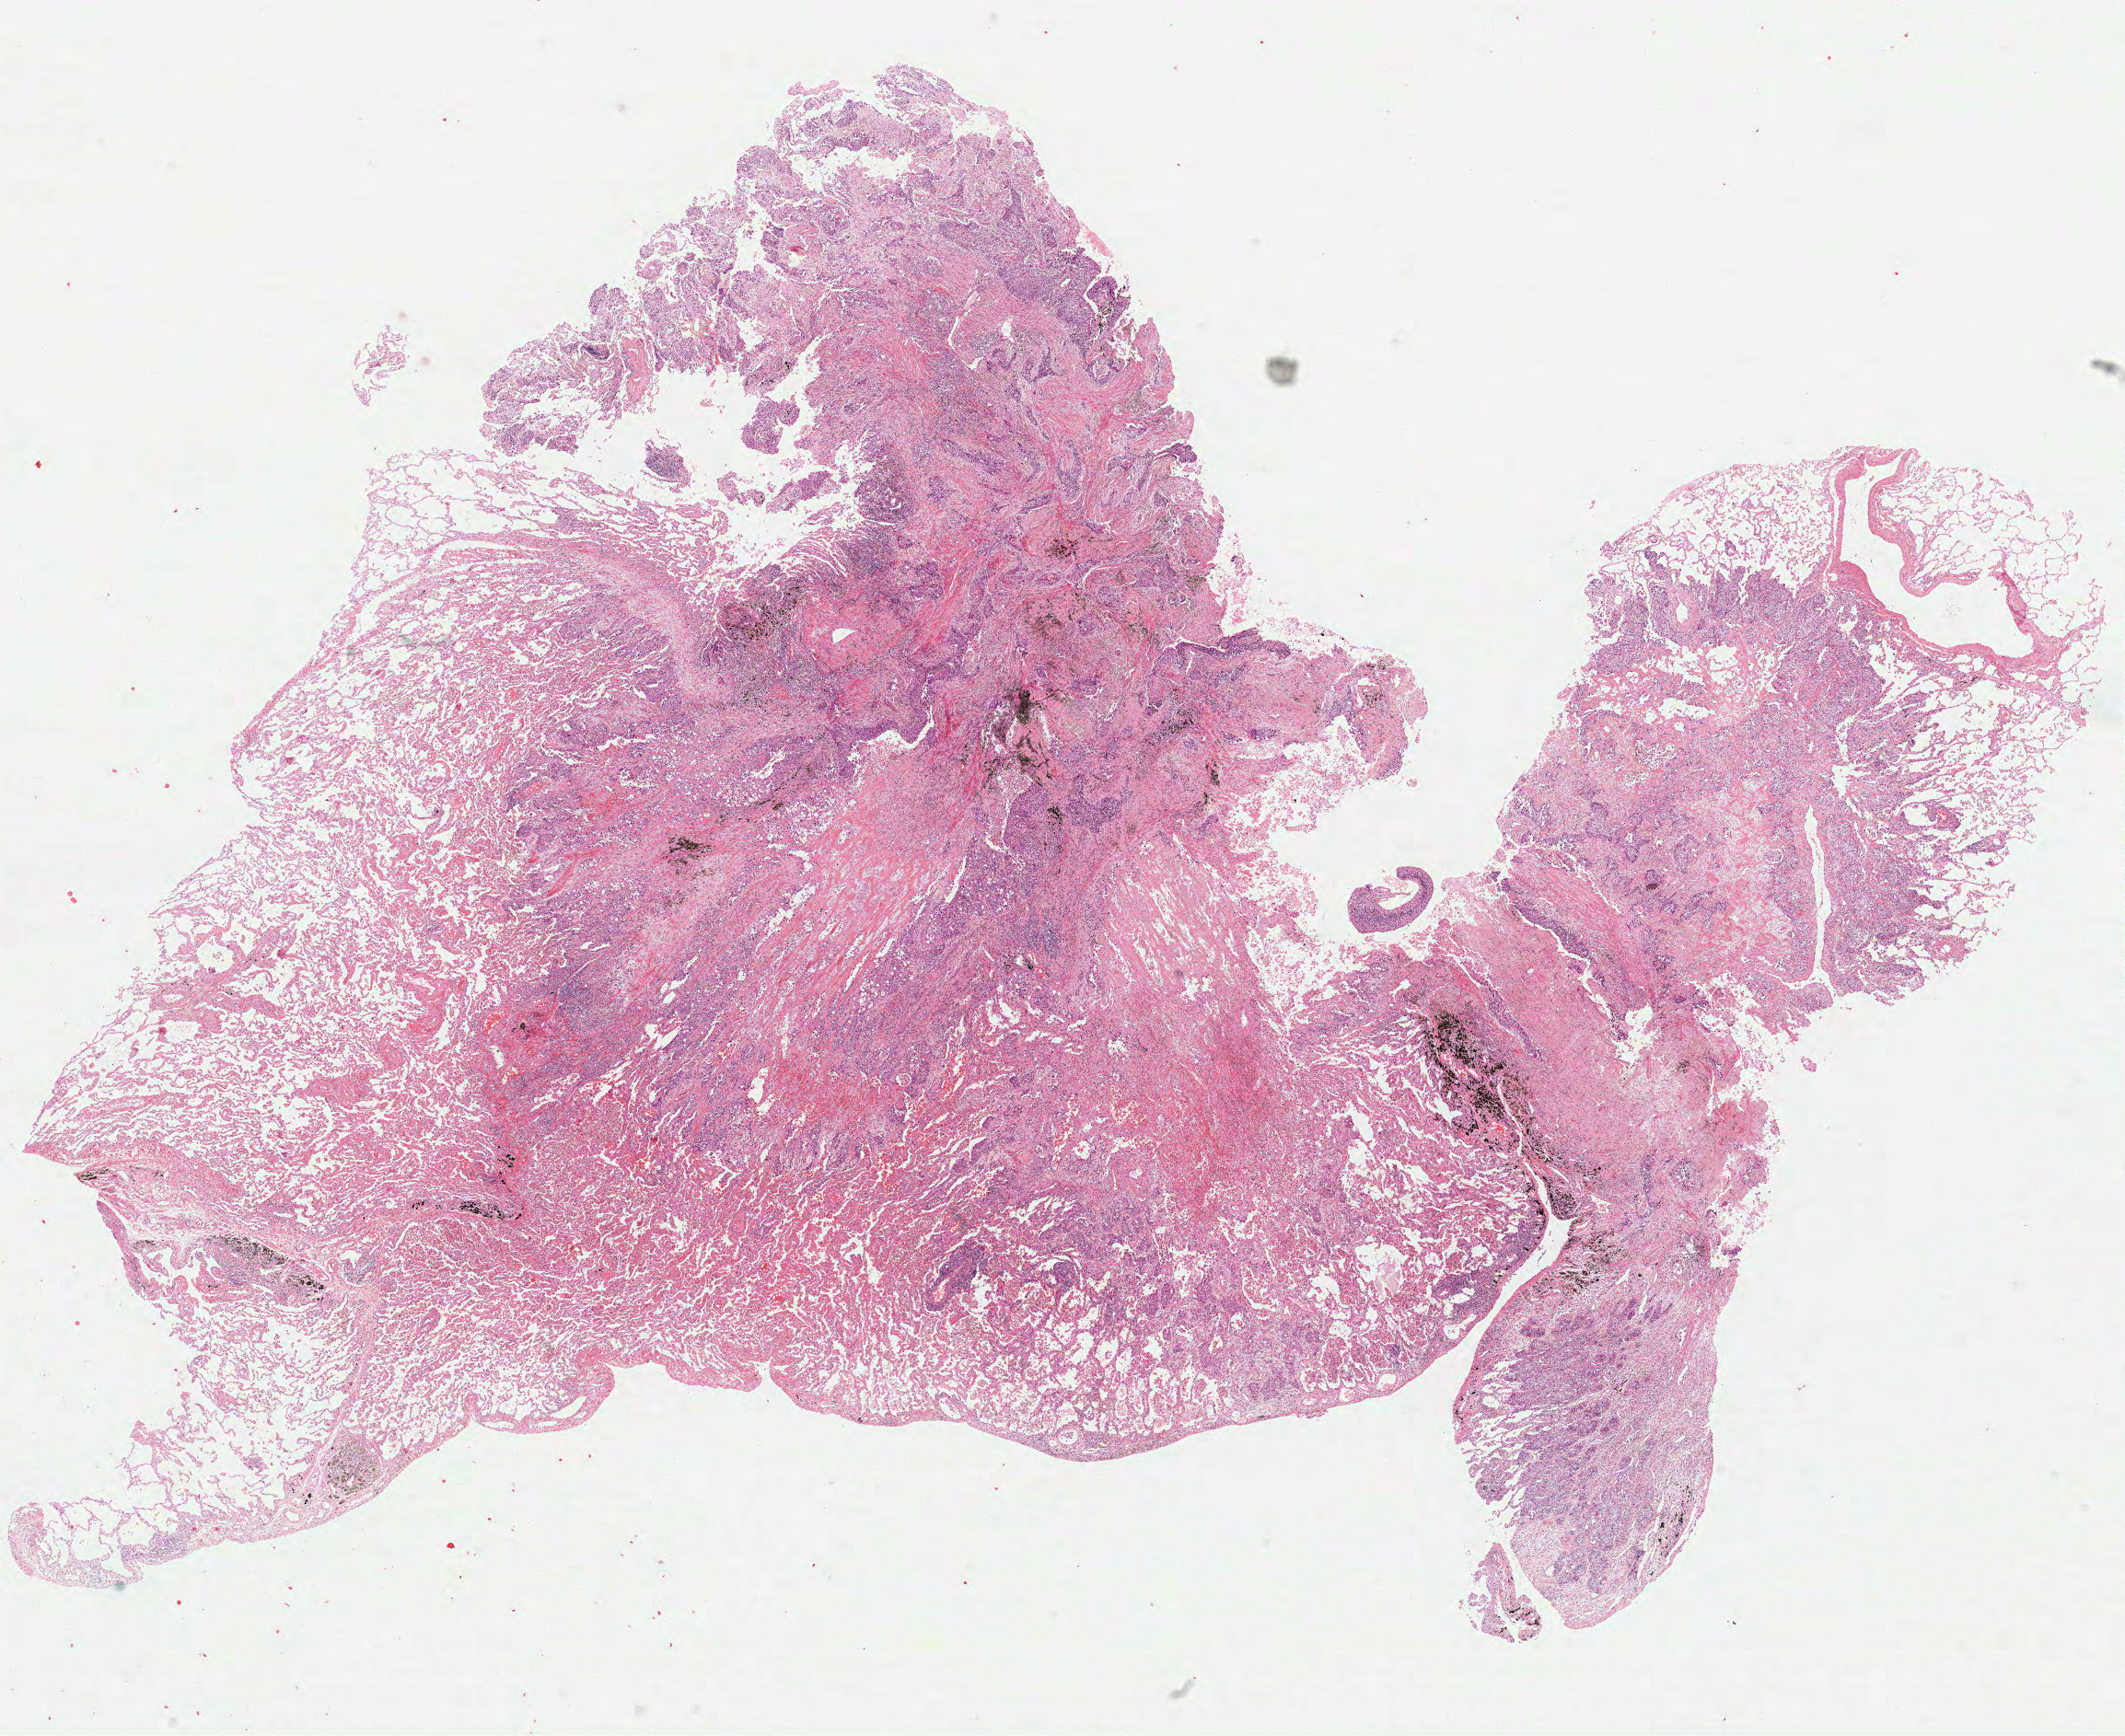
Whole-slide histology image, H&E — low-resolution overview of the scanned area, about 18.6 x 15.2 mm (acquisition: 40x scan). FFPE section. Sample: primary tumour, lung. Patient: male, age at initial diagnosis 61 years.
* TNM: T1b N0 M0
* AJCC pathologic stage: IA
* histologic diagnosis: Squamous cell carcinoma, NOS
* laterality: right